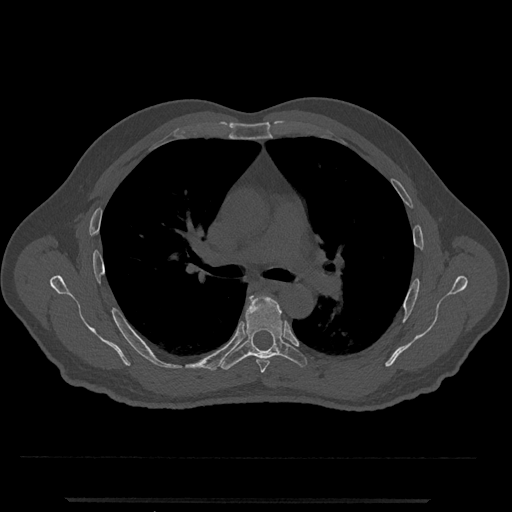
CT including the spine, one axial slice. Position 756 of 797 along the scan axis. Reconstruction kernel Br40s/3. 120 kVp. Bone window (W 1800 / L 400 HU). 512 × 512 image matrix, field of view 419 × 419 mm. Patient: male, 63 years. Case-level facts recorded for this patient, not image findings: primary cancer: prostate.
Outlined on this slice (semi-automatically segmented with operator editing):
- T5 vertebra: bounding box <247,306,270,373> (left, top, right, bottom; pixels)
- T6 vertebra: <219,294,307,370>